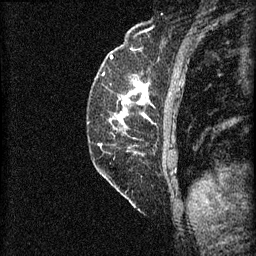
Breast MRI (dynamic contrast-enhanced), one sagittal slice; 3 images stored at this slice position (order not interpretable as contrast timing); 1.5 T; TE 4.2 ms, TR 8.2 ms; 256 × 256 image matrix, field of view 180 × 180 mm. Female patient, age 59 years.
Structures marked on this image (semi-automatic segmentation, software-assisted and operator-edited):
- analysis volume of interest (the breast-tissue region the enhancement analysis was run in; not a lesion): bounding box [x1, y1, x2, y2] px = [96, 74, 155, 131]
- tumour enhancement mask (voxels above the 70 % enhancement threshold inside the analysis volume of interest): [120, 82, 149, 117]